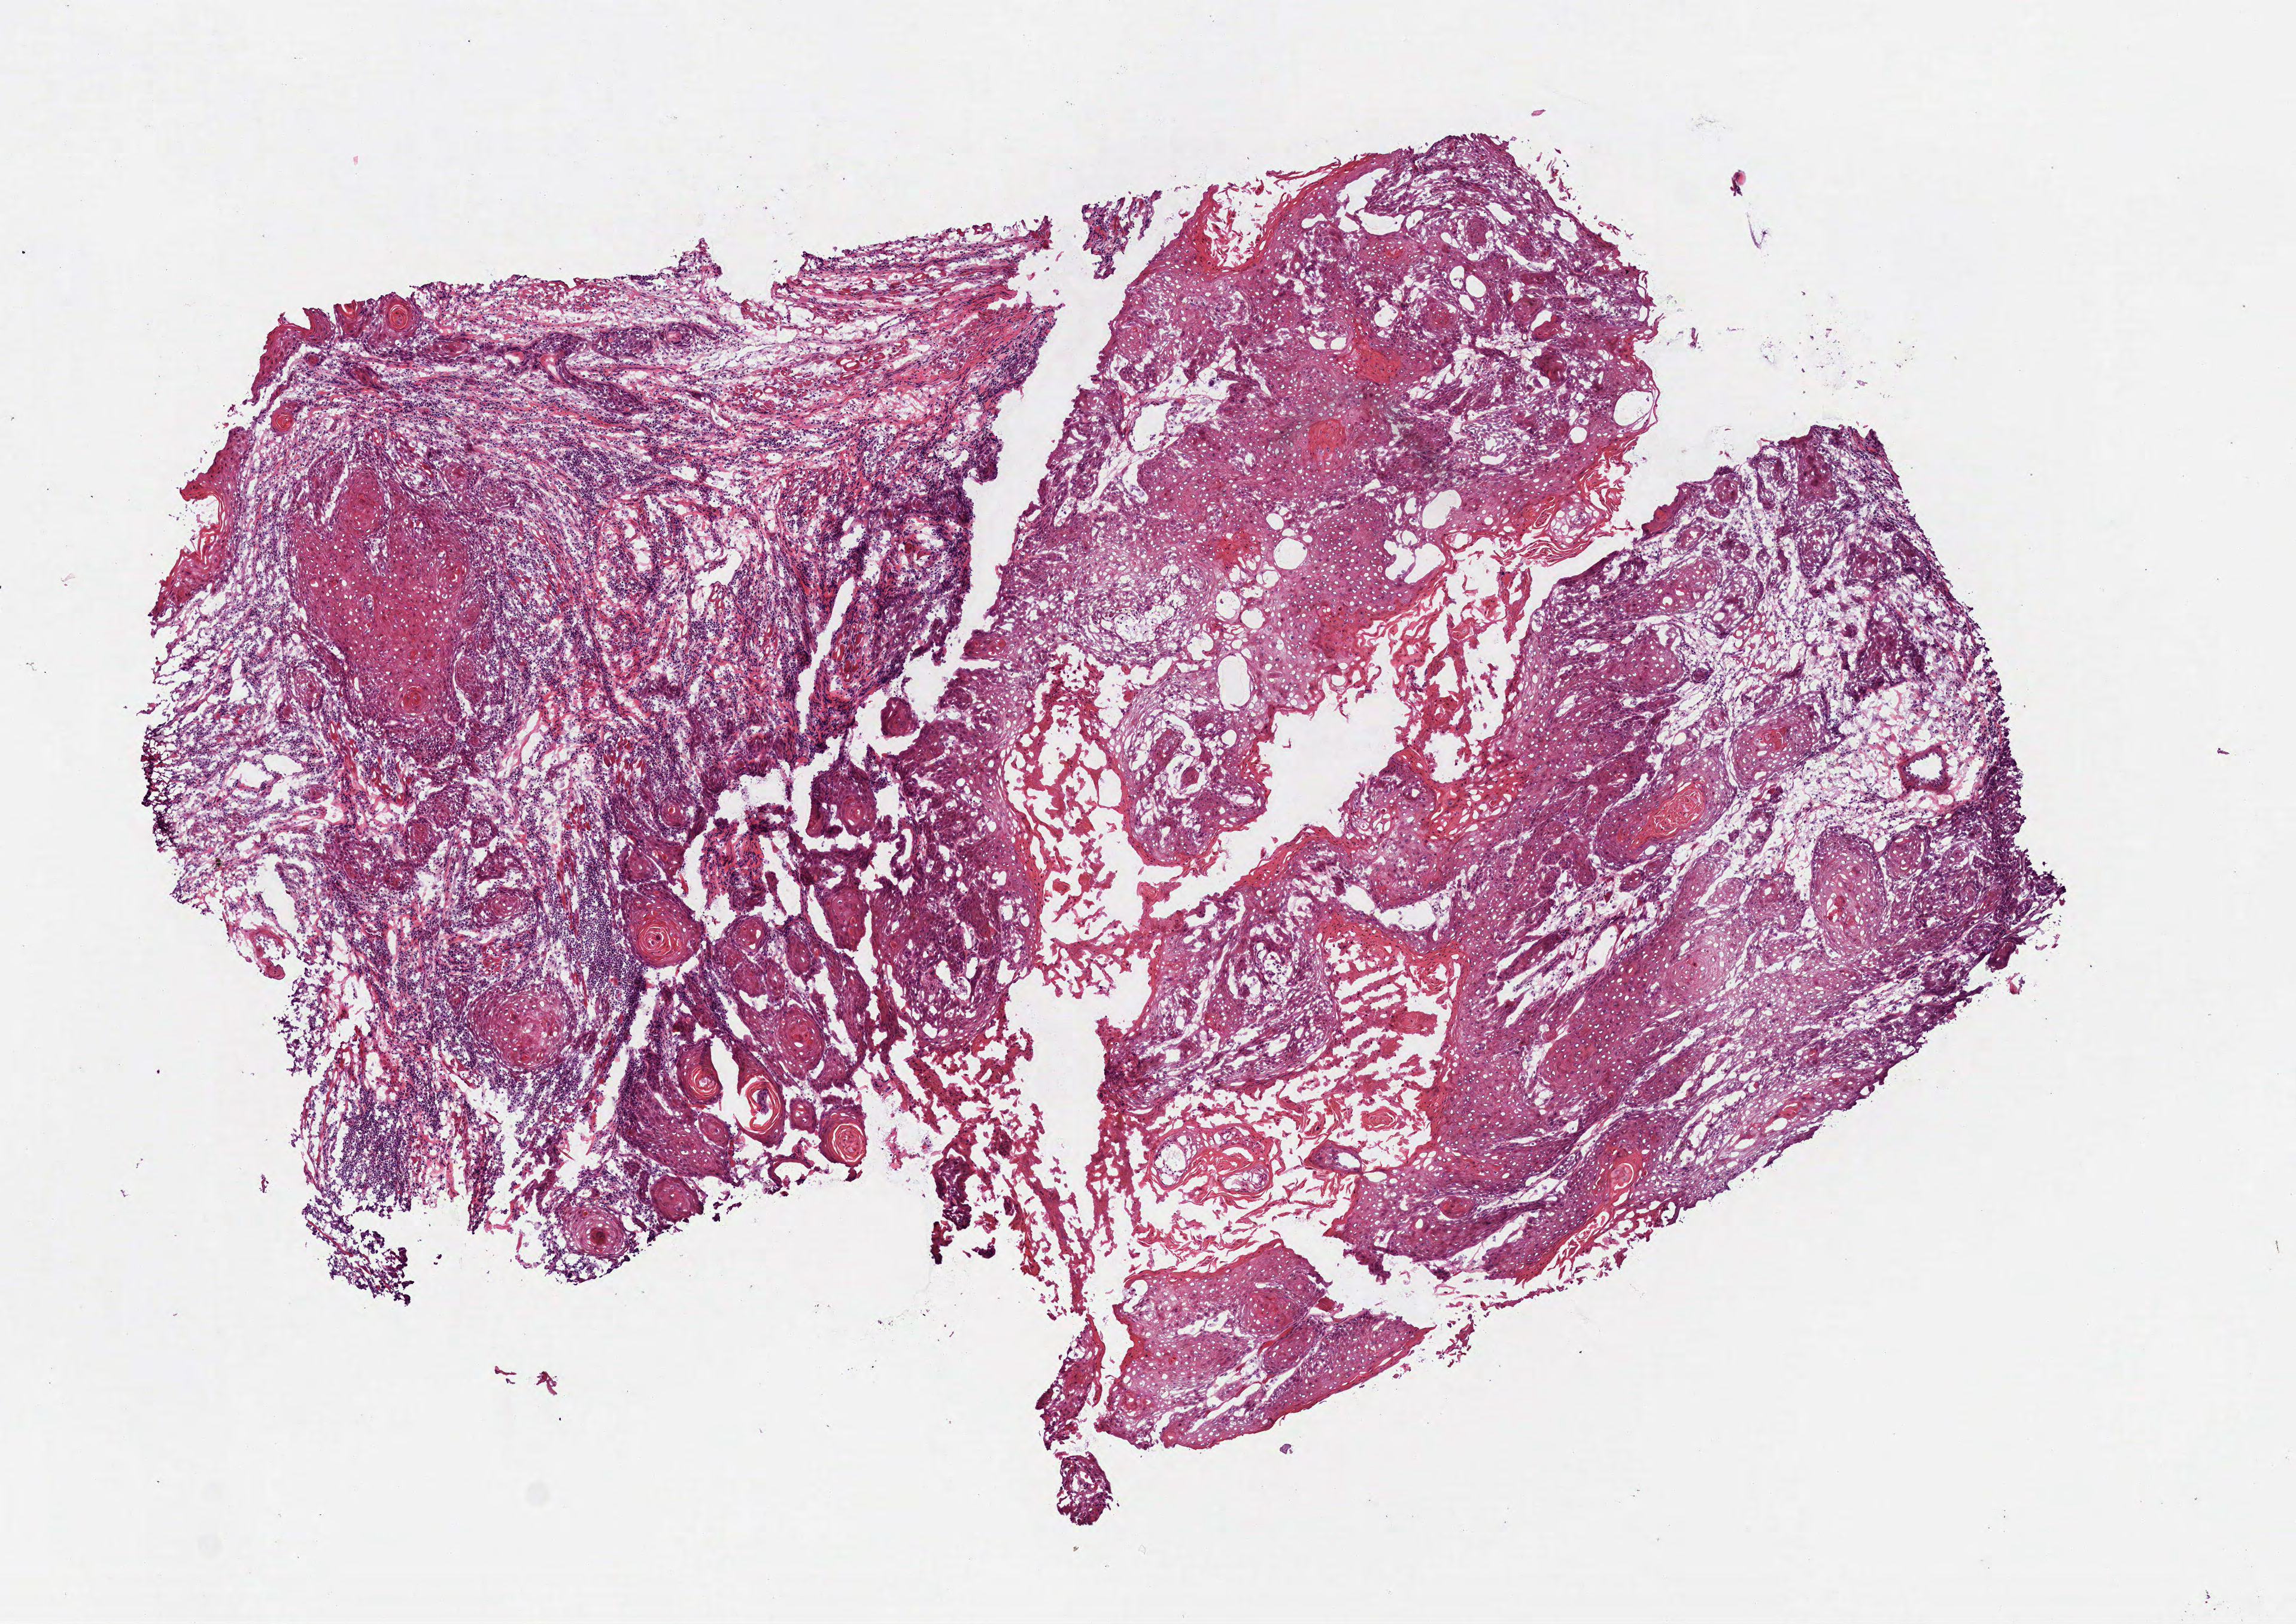
Digitized H&E-stained tissue section (whole slide), shown as a low-resolution overview of the whole scanned area (about 7.7 x 5.5 mm, from a 40x scan), frozen section from the bottom of the tissue portion, head and neck, primary tumour sample. Female, age 65 years at initial diagnosis. Histologic grade: G1 (well differentiated). Slide review estimates, as recorded: tumour cells 75%, tumour nuclei 50%, normal cells 0%, stromal cells 20%, necrosis 5%. Inflammatory infiltration, as recorded: lymphocyte infiltration 30%, monocyte infiltration 0%, neutrophil infiltration 10%.
Pathologic diagnosis: Squamous cell carcinoma, NOS (tongue, NOS). AJCC pathologic stage: IVA (7th edition).